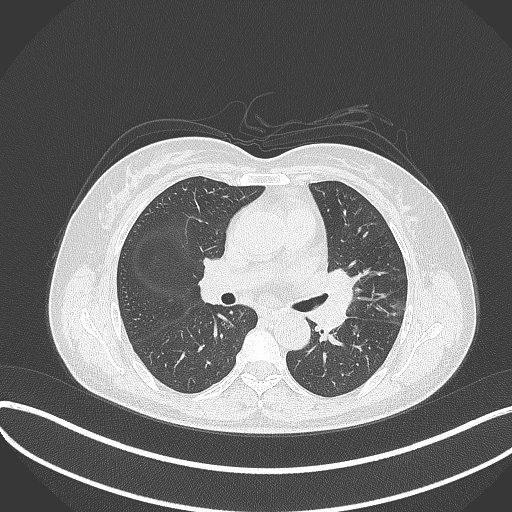
Chest CT, one axial slice. Position 197 of 373 along the scan axis. Reconstruction kernel B70f. 120 kVp. Lung window (W 1500 / L -600 HU). 1 mm slice thickness. 512 × 512 image matrix, field of view 400 × 400 mm. Female patient, age 54 years. Case-level facts recorded for this patient, not image findings: clinical TNM (as recorded): T2a N1 M0; histopathological grade: G3.
Annotated regions visible in this slice (bounding box drawn by a radiologist):
- lung tumour (recorded histology: small cell carcinoma): bounding box (x1, y1, x2, y2) in pixels: (313, 267, 355, 334)